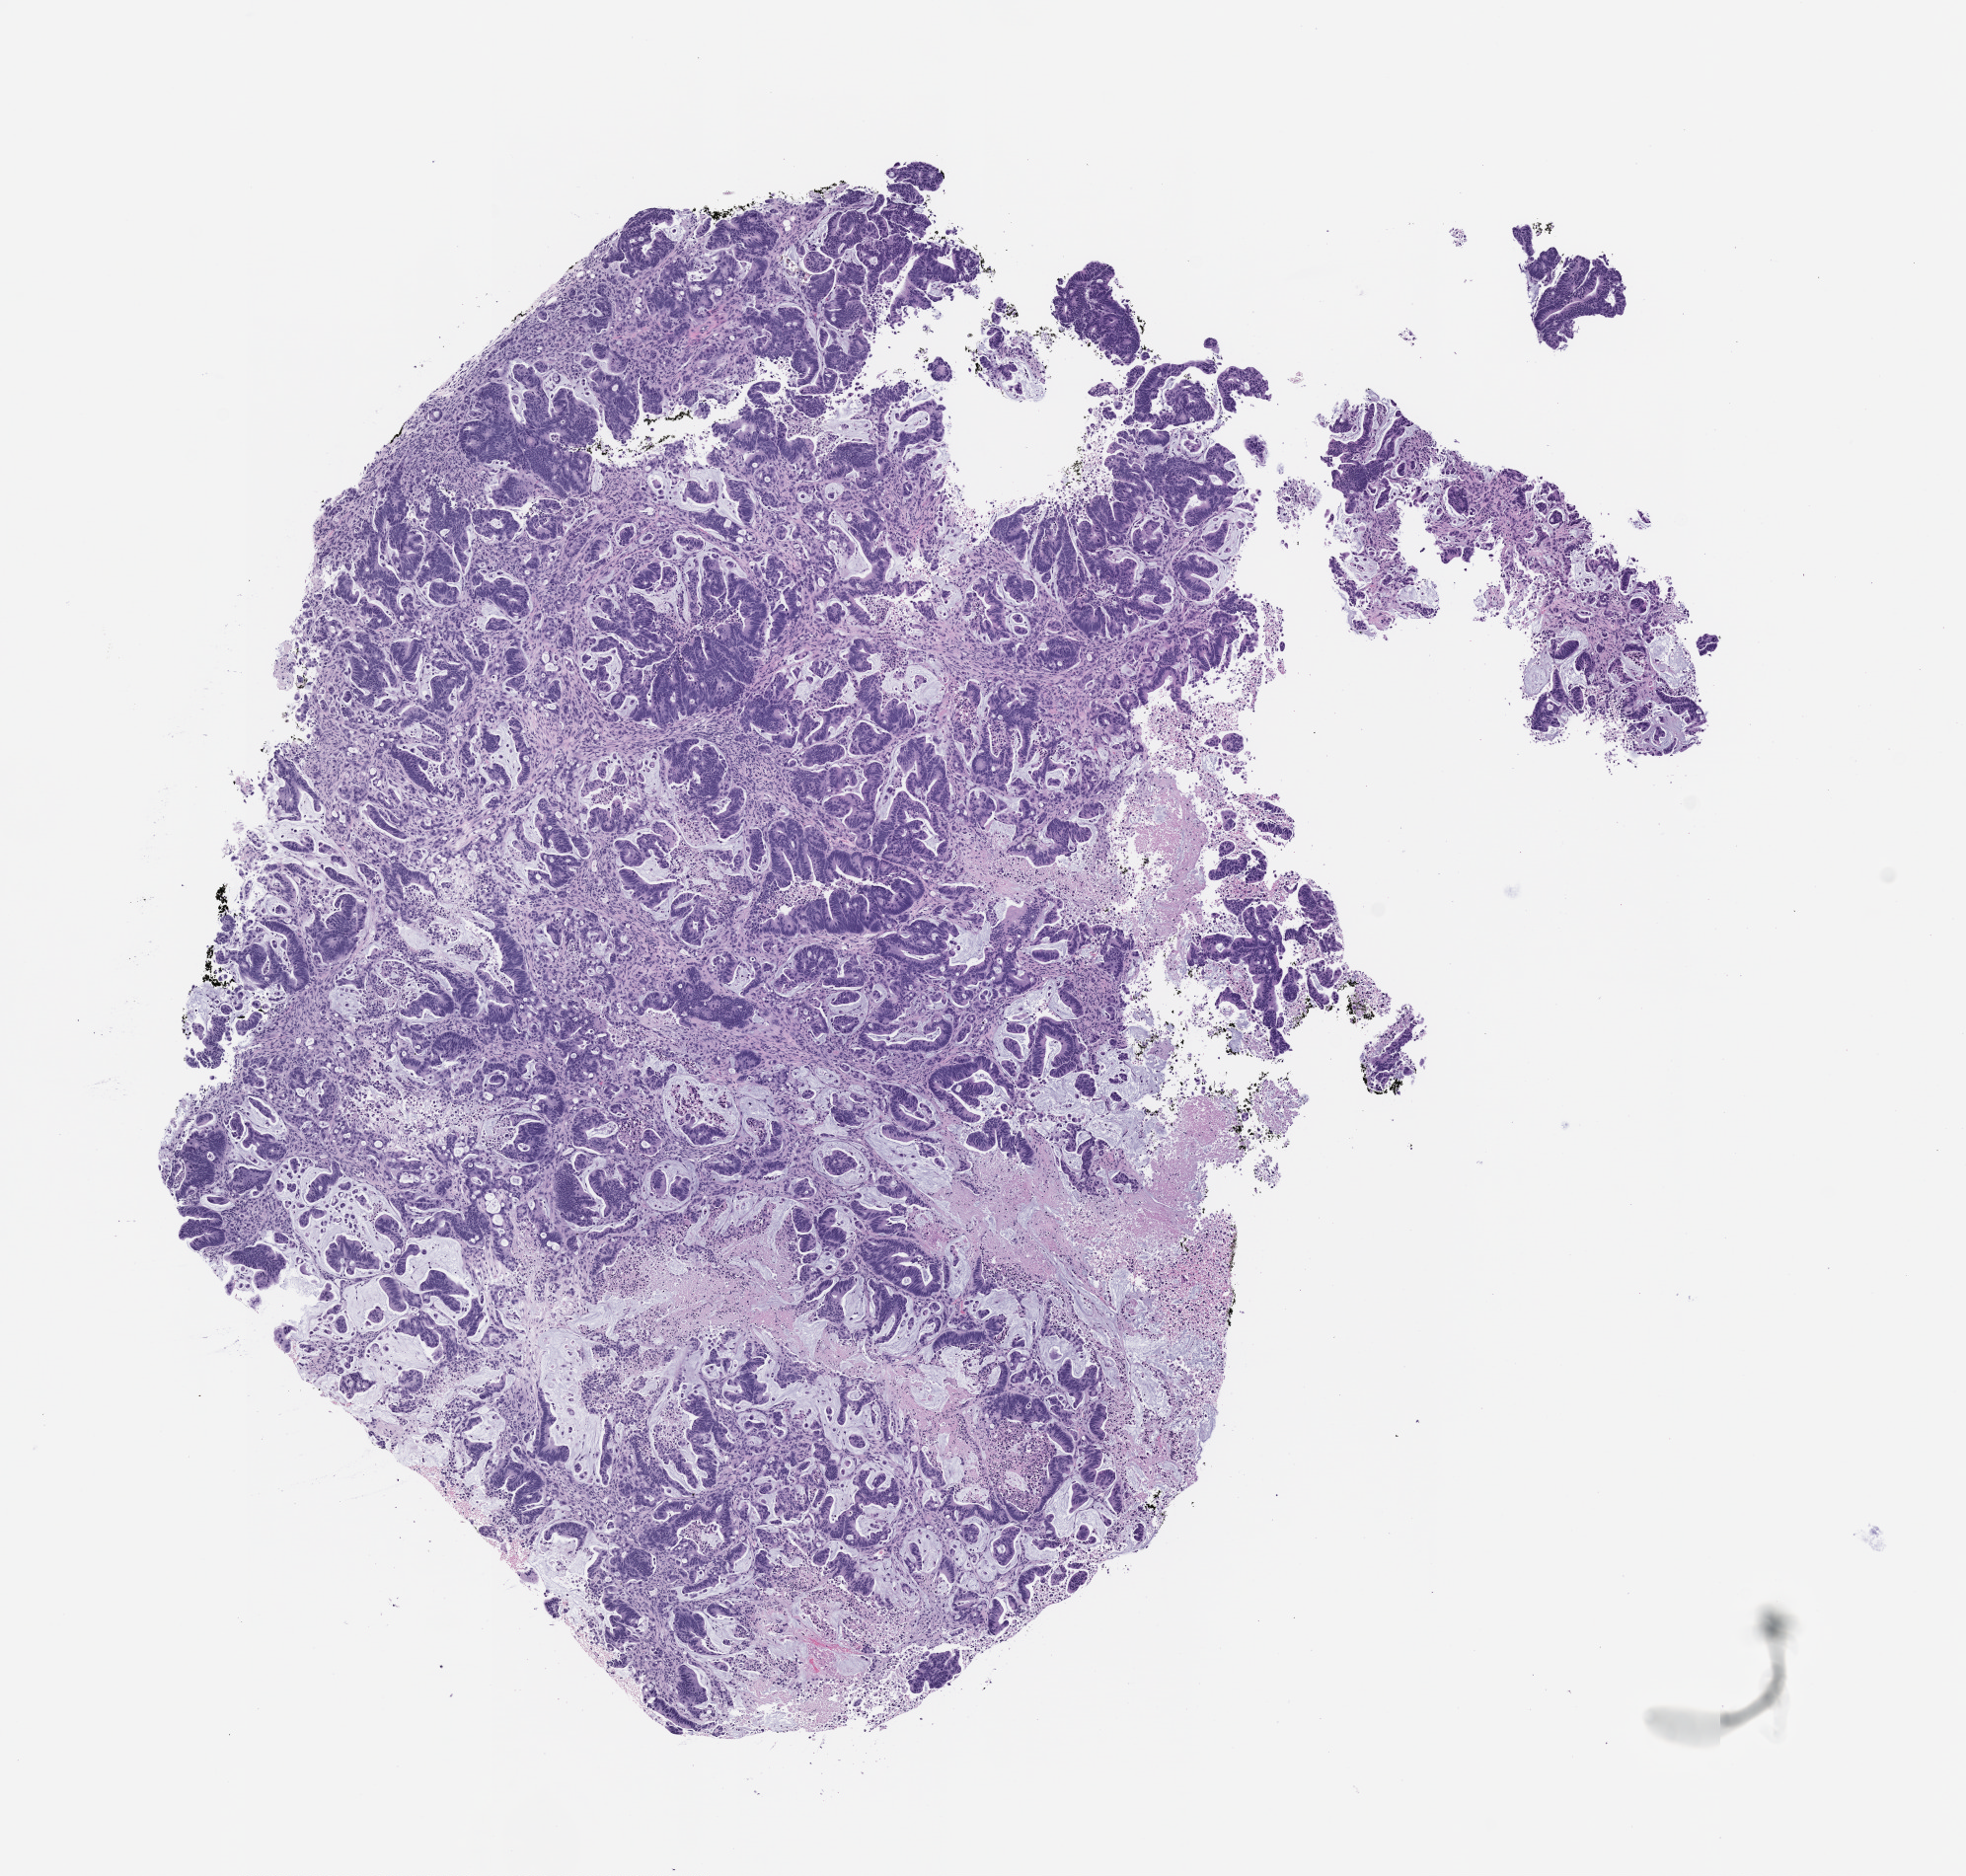
Haematoxylin and eosin whole-slide image of a patient-derived xenograft (PDX) tumor grown in a mouse, passage 1, low-resolution overview of the scanned area, about 8.0 x 7.6 mm. Formalin-fixed paraffin-embedded section. Originating tumor site category: colon.
Originating patient diagnosis: Colon Adenocarcinoma.